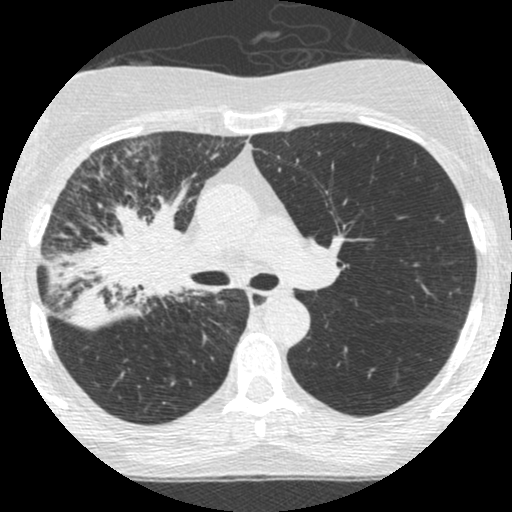
Low-dose screening chest CT, one axial slice. Position 164 of 253 along the scan axis. Reconstruction kernel STANDARD. 120 kVp. Lung window (W 1500 / L -600 HU). 512 × 512 image matrix.
Structures marked on this image (outlined manually by an expert reader):
- lesion 2 (tumor, hilum of right lung): bounding box (x1, y1, x2, y2) in pixels: (45, 189, 186, 328)